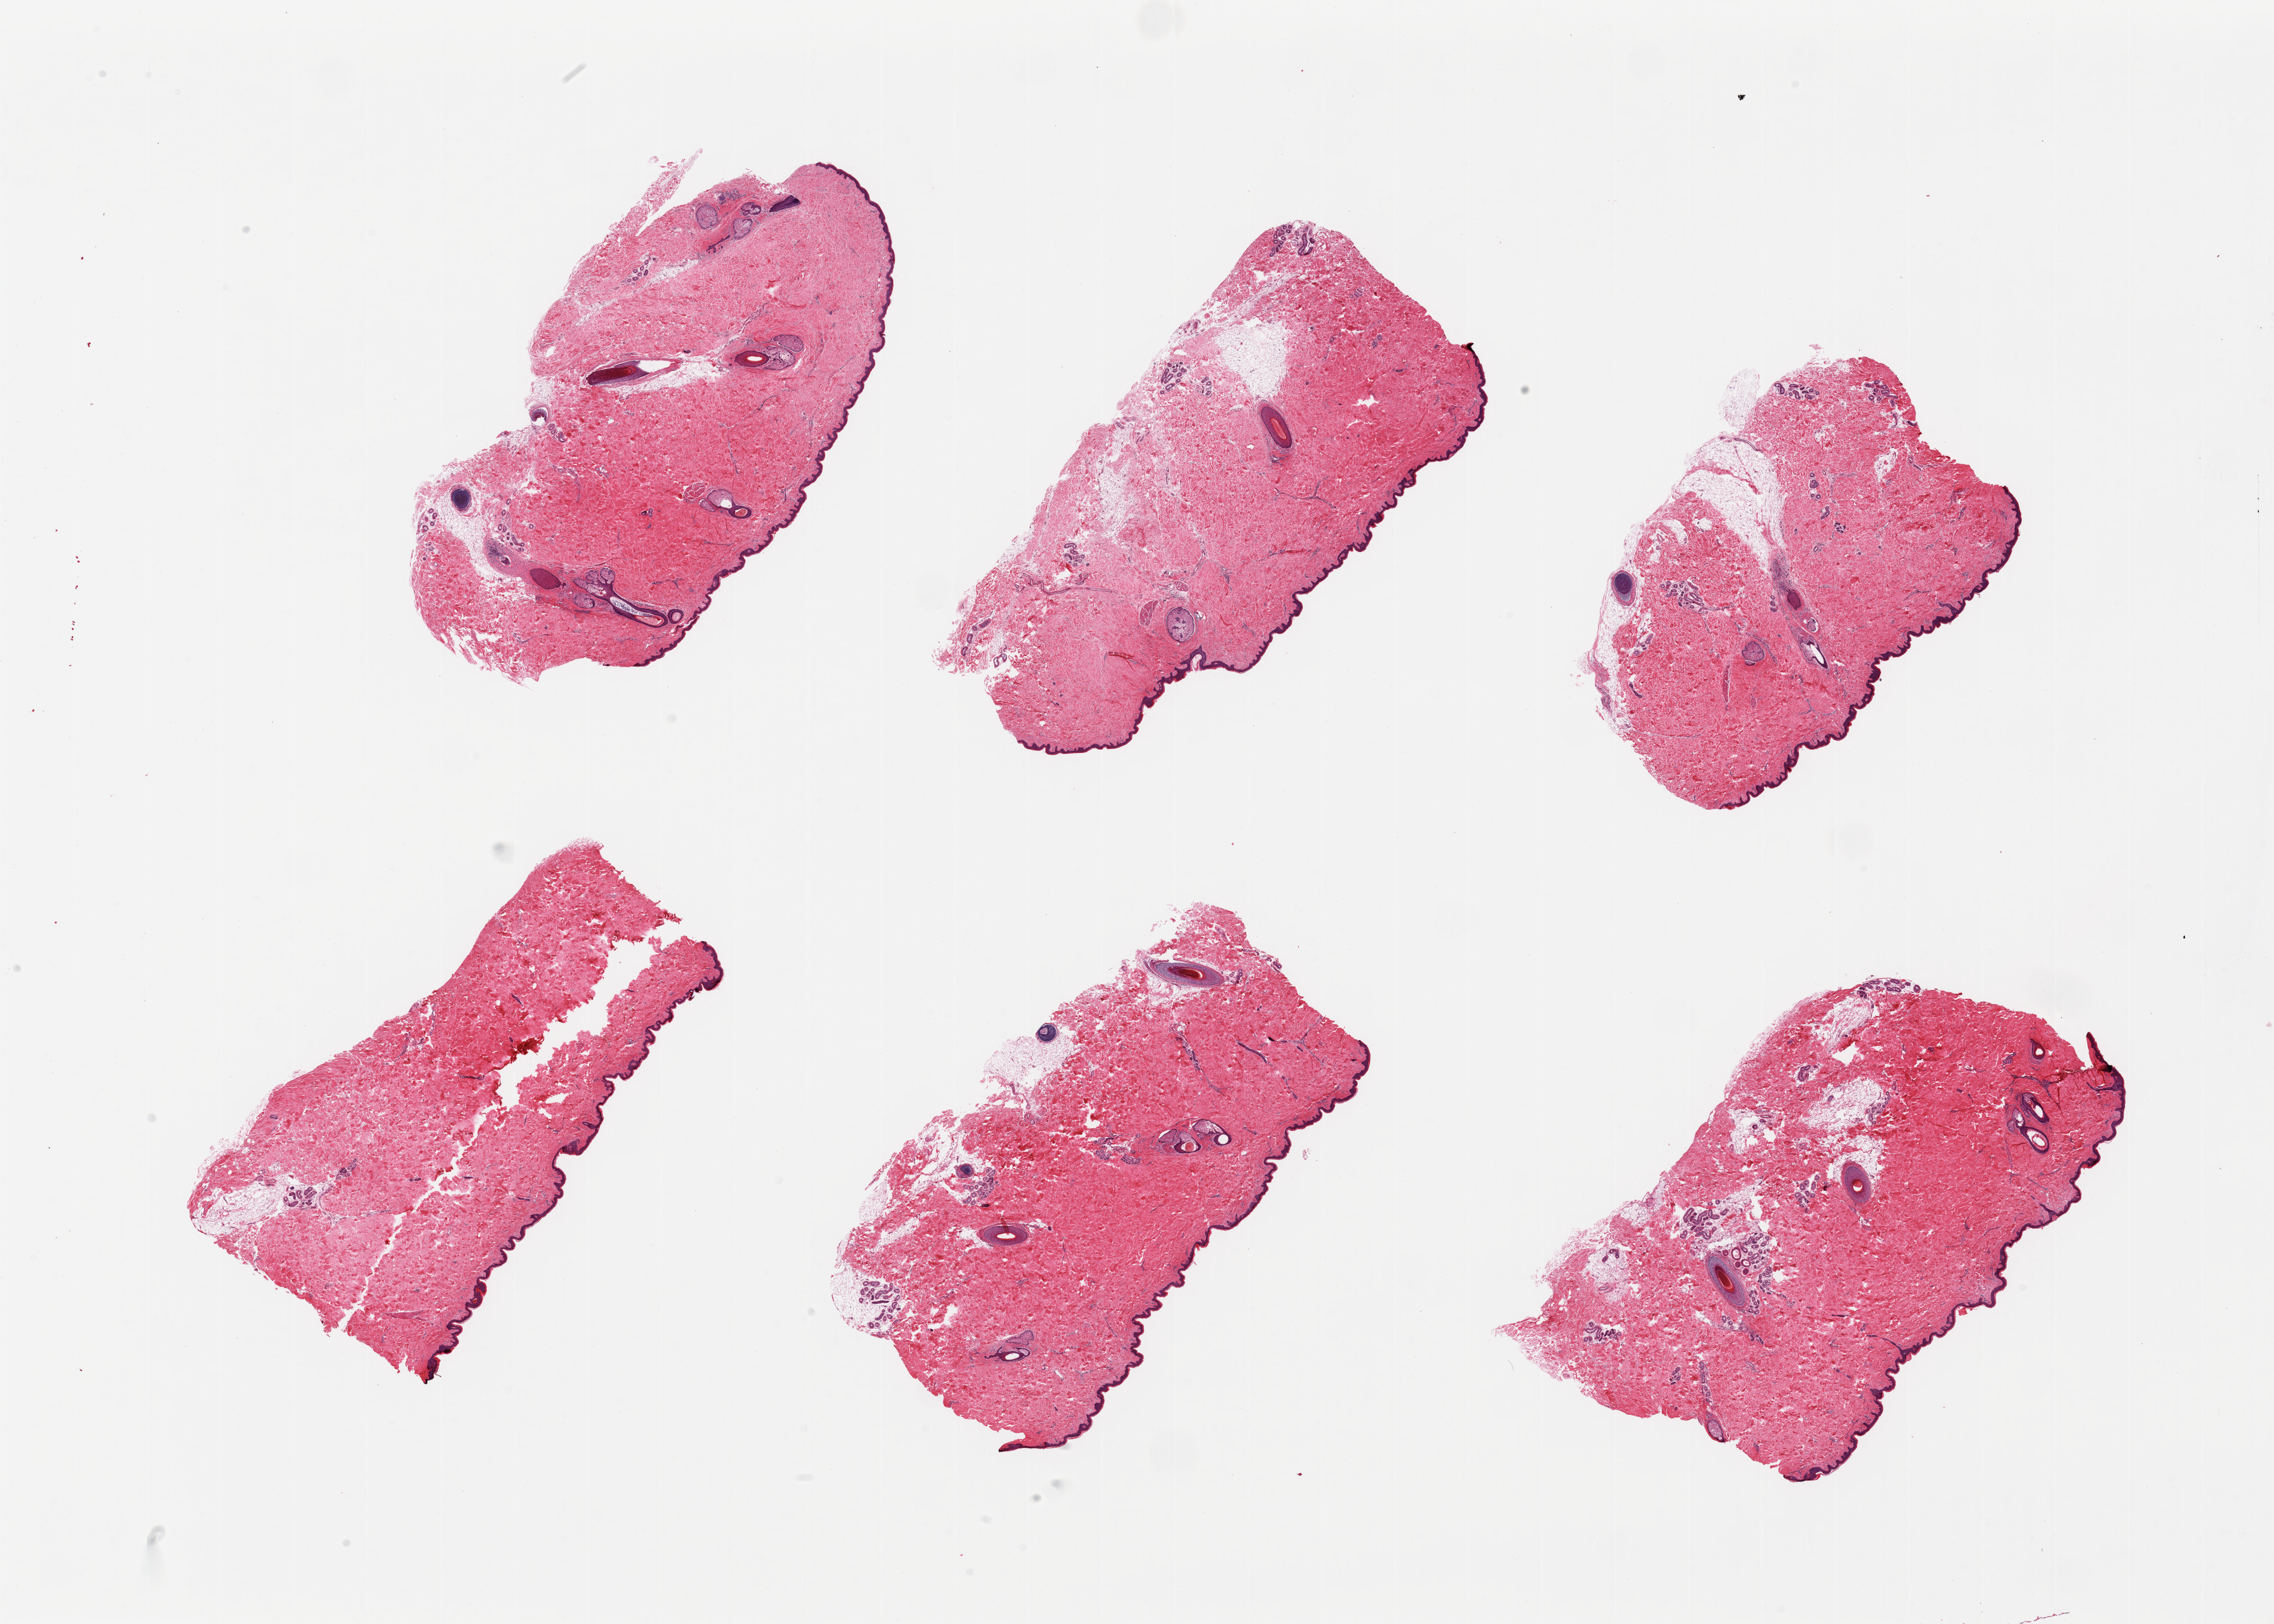
Whole-slide image, hematoxylin and eosin (H&E) stain, low-resolution overview of the scanned area, about 30.5 x 21.8 mm (acquisition: 20x scan), PAXgene-fixed paraffin-embedded (PFPE) section, sampled site (target tissue): skin of suprapubic region, tissue donor sample. Donor: male.
Pathologist's review note for this sample: 6 pieces; hair bearing skin; mostly periadnexal fat.